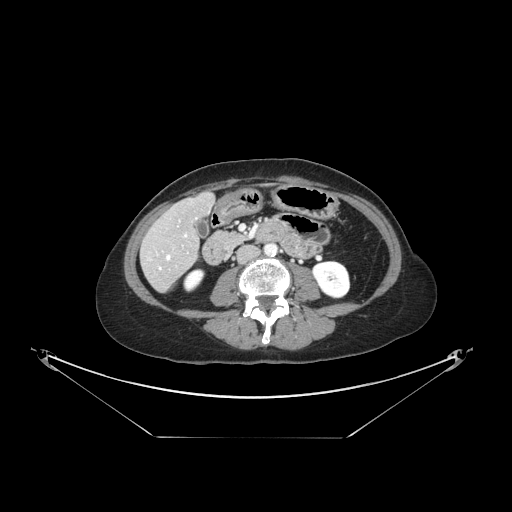
Contrast-enhanced abdominal CT, one axial slice. Position 43 of 148 along the scan axis. Soft-tissue window (W 400 / L 40 HU). 2.5 mm slice thickness. 512 × 512 image matrix, field of view 500 × 500 mm. Female patient, age 73 years. Case-level facts recorded for this patient, not image findings: diagnosis: colorectal cancer liver metastases, imaged before liver resection; multiple liver metastases: no.
Structures marked on this image (expert manual segmentation):
- hepatic veins: bounding box [x1, y1, x2, y2] px = [159, 235, 187, 269]
- liver: [143, 195, 214, 291]
- planned liver remnant (the part of the liver to remain after resection): [161, 196, 214, 242]